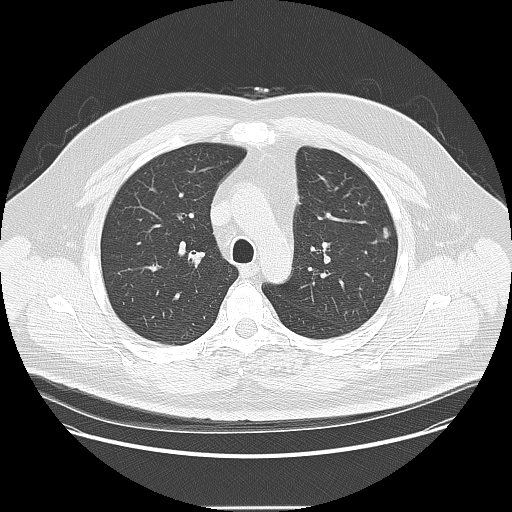
Low-dose screening chest CT, one axial slice; position 109 of 157 along the scan axis; reconstruction kernel LUNG; 120 kVp; lung window (W 1500 / L -600 HU); 512 × 512 image matrix.
Annotated regions visible in this slice (outlined manually by an expert reader):
- lesion 1 (tumor, upper lobe of left lung): bounding box [x1, y1, x2, y2] px = [383, 227, 390, 239]